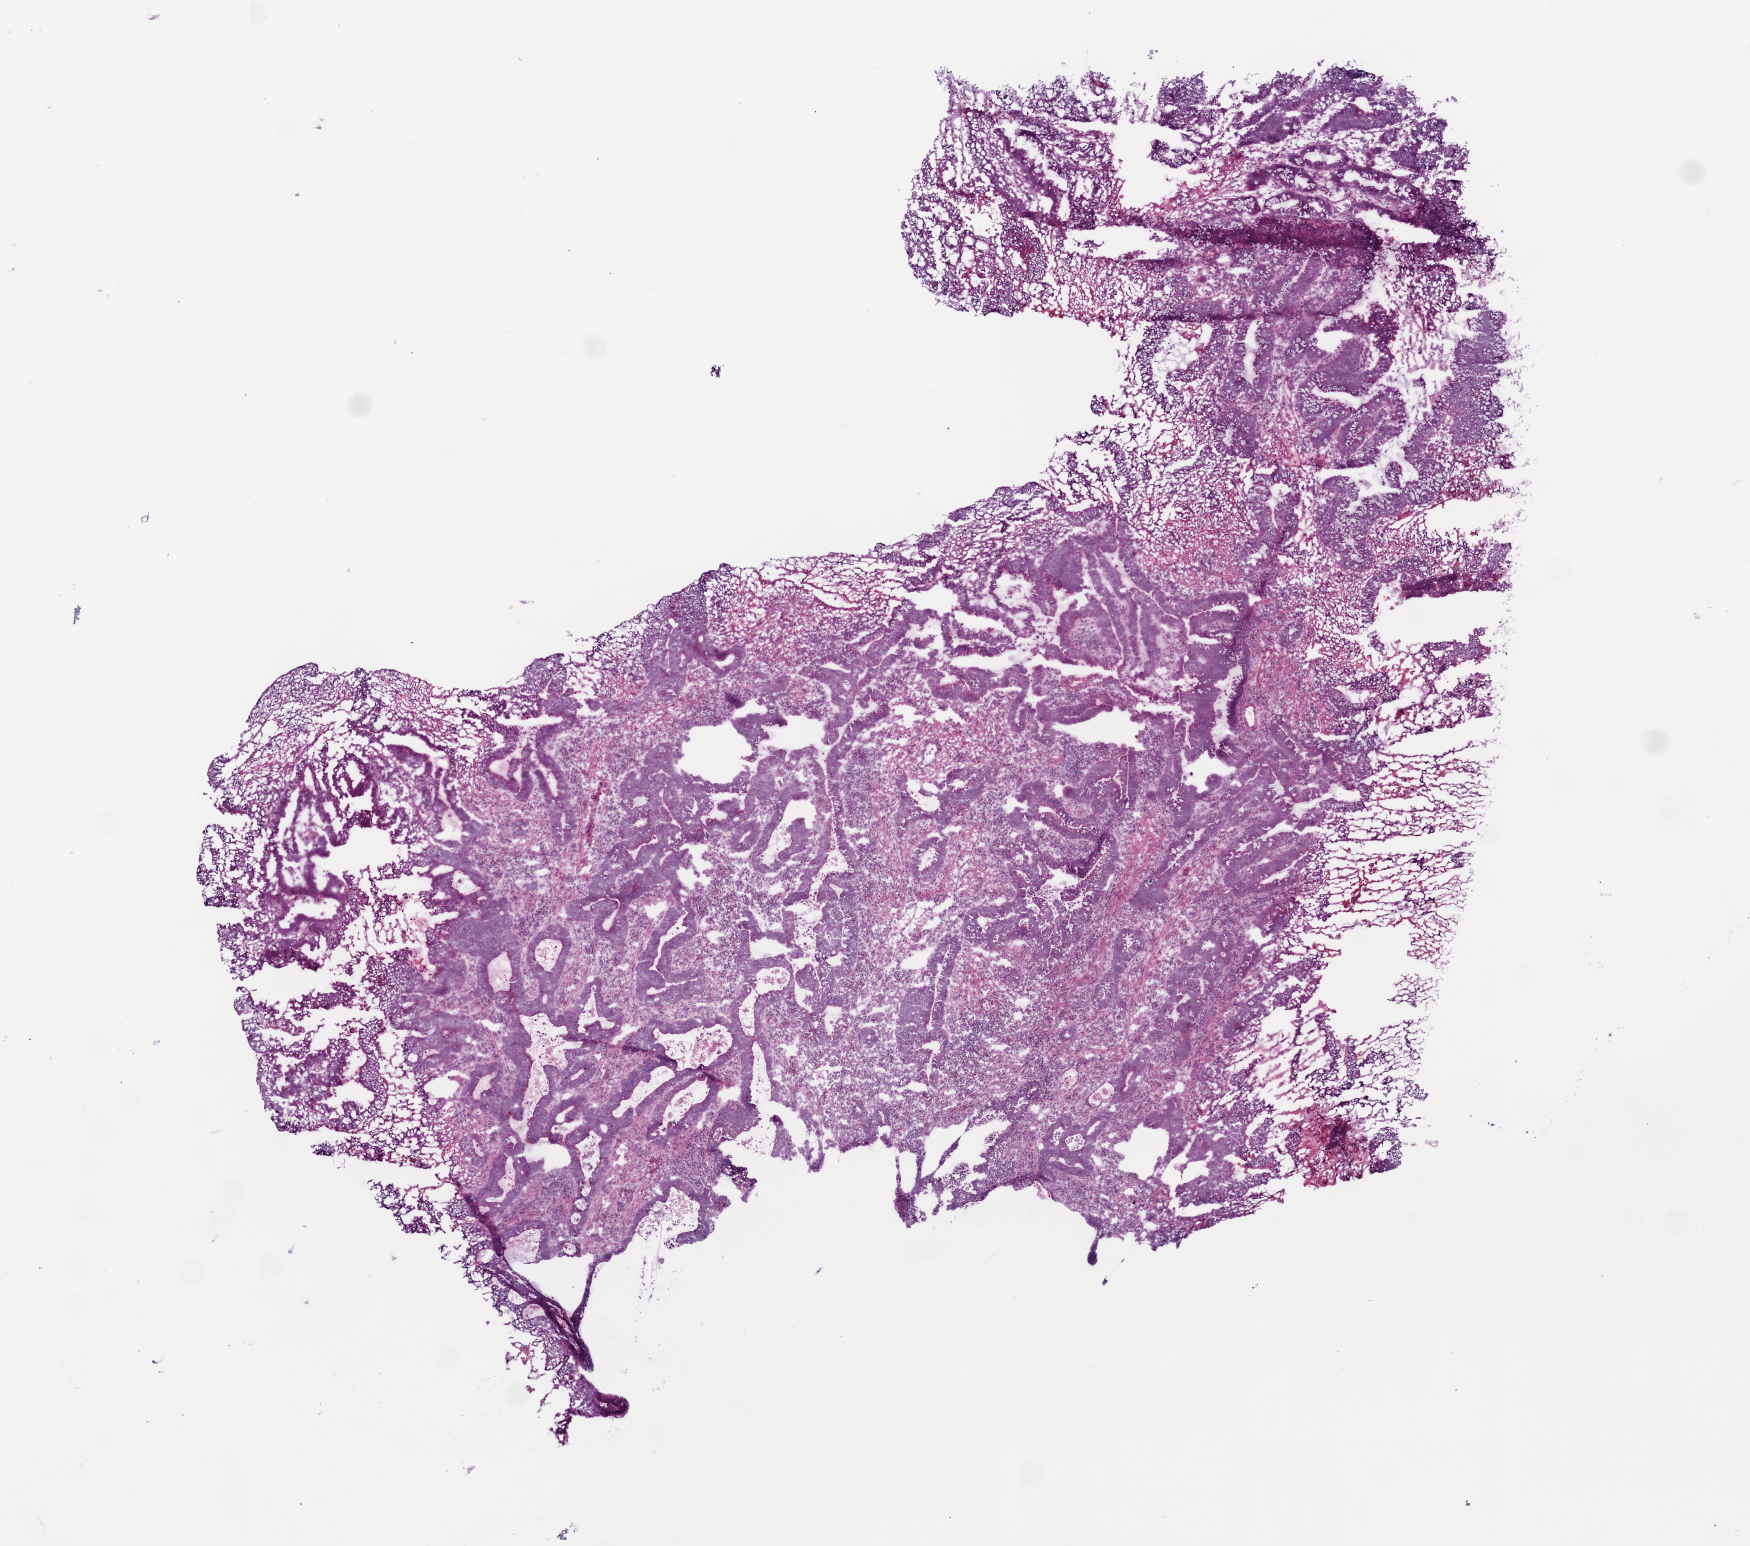
Digitized Hematoxylin and eosin (H&E) stained tissue section (whole slide), low-resolution overview of the scanned area, about 7.0 x 6.2 mm (from a 20x scan), frozen section from the bottom of the tissue portion, rectum, primary tumour sample. Male, age 62 years at initial diagnosis. Pathologist review of this section (percent, as recorded): tumour cells 72%, tumour nuclei 70%, normal cells 0%, stromal cells 20%, necrosis 8%.
AJCC pathologic stage: I (6th edition). Lymph nodes positive (case pathology): 0 of 12 examined. Diagnosis: Adenocarcinoma, NOS. TNM: T2 N0 M0.